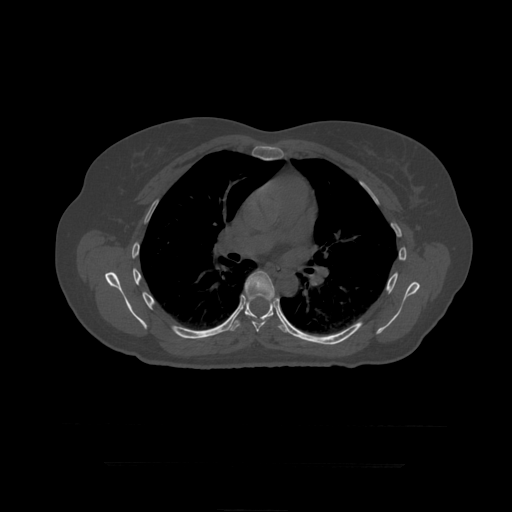
CT including the spine, one axial slice. Position 293 of 399 along the scan axis. Reconstruction kernel STANDARD. 120 kVp. Bone window (W 1800 / L 400 HU). 512 × 512 image matrix, field of view 450 × 450 mm. Patient age 41 years. From the clinical record (not read from this slice): primary cancer: breast.
Structures marked on this image (semi-automatic segmentation, software-assisted and operator-edited):
- T7 vertebra: bounding box <243,270,278,332> (left, top, right, bottom; pixels)
- T8 vertebra: <230,297,285,333>